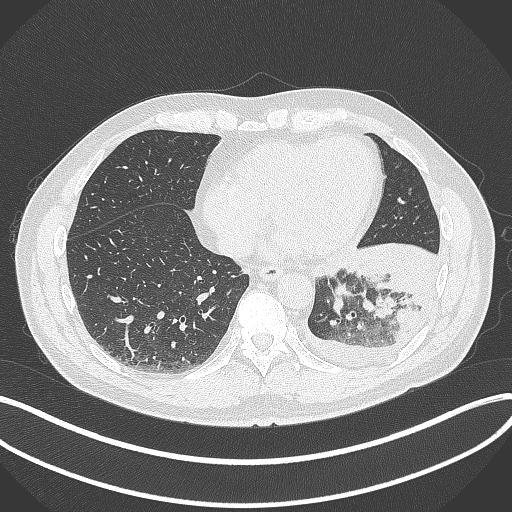
Chest CT, one axial slice. Slice 108 of 342 in the series (ordered by position). Lung window (W 1500 / L -600 HU). 1 mm slice thickness. 512 × 512 image matrix, field of view 400 × 400 mm. Patient: male, 58 years. Case-level facts recorded for this patient, not image findings: clinical TNM (as recorded): T3 N1 M1b; histopathological grade: G3.
Outlined on this slice (bounding box drawn by a radiologist):
- lung tumour (recorded histology: small cell carcinoma): bounding box <326,269,352,321> (left, top, right, bottom; pixels)